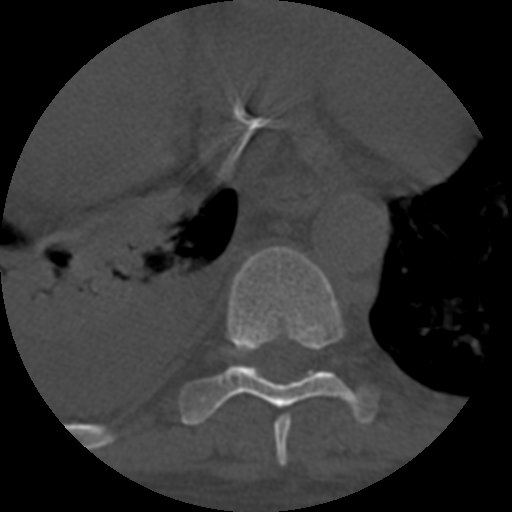
CT including the spine, one axial slice; position 377 of 708 along the scan axis; reconstruction kernel STANDARD; 120 kVp; one of 3 acquisitions stored at this slice position; bone window (W 1800 / L 400 HU); 1.25 mm slice thickness; 512 × 512 image matrix, field of view 160 × 160 mm. Patient age 55 years. Case-level facts recorded for this patient, not image findings: primary cancer: colon.
Annotated regions visible in this slice (semi-automatically segmented with operator editing):
- T10 vertebra: bounding box (x1, y1, x2, y2) in pixels: (229, 346, 251, 357)
- T8 vertebra: (273, 415, 291, 466)
- T9 vertebra: (180, 246, 377, 426)